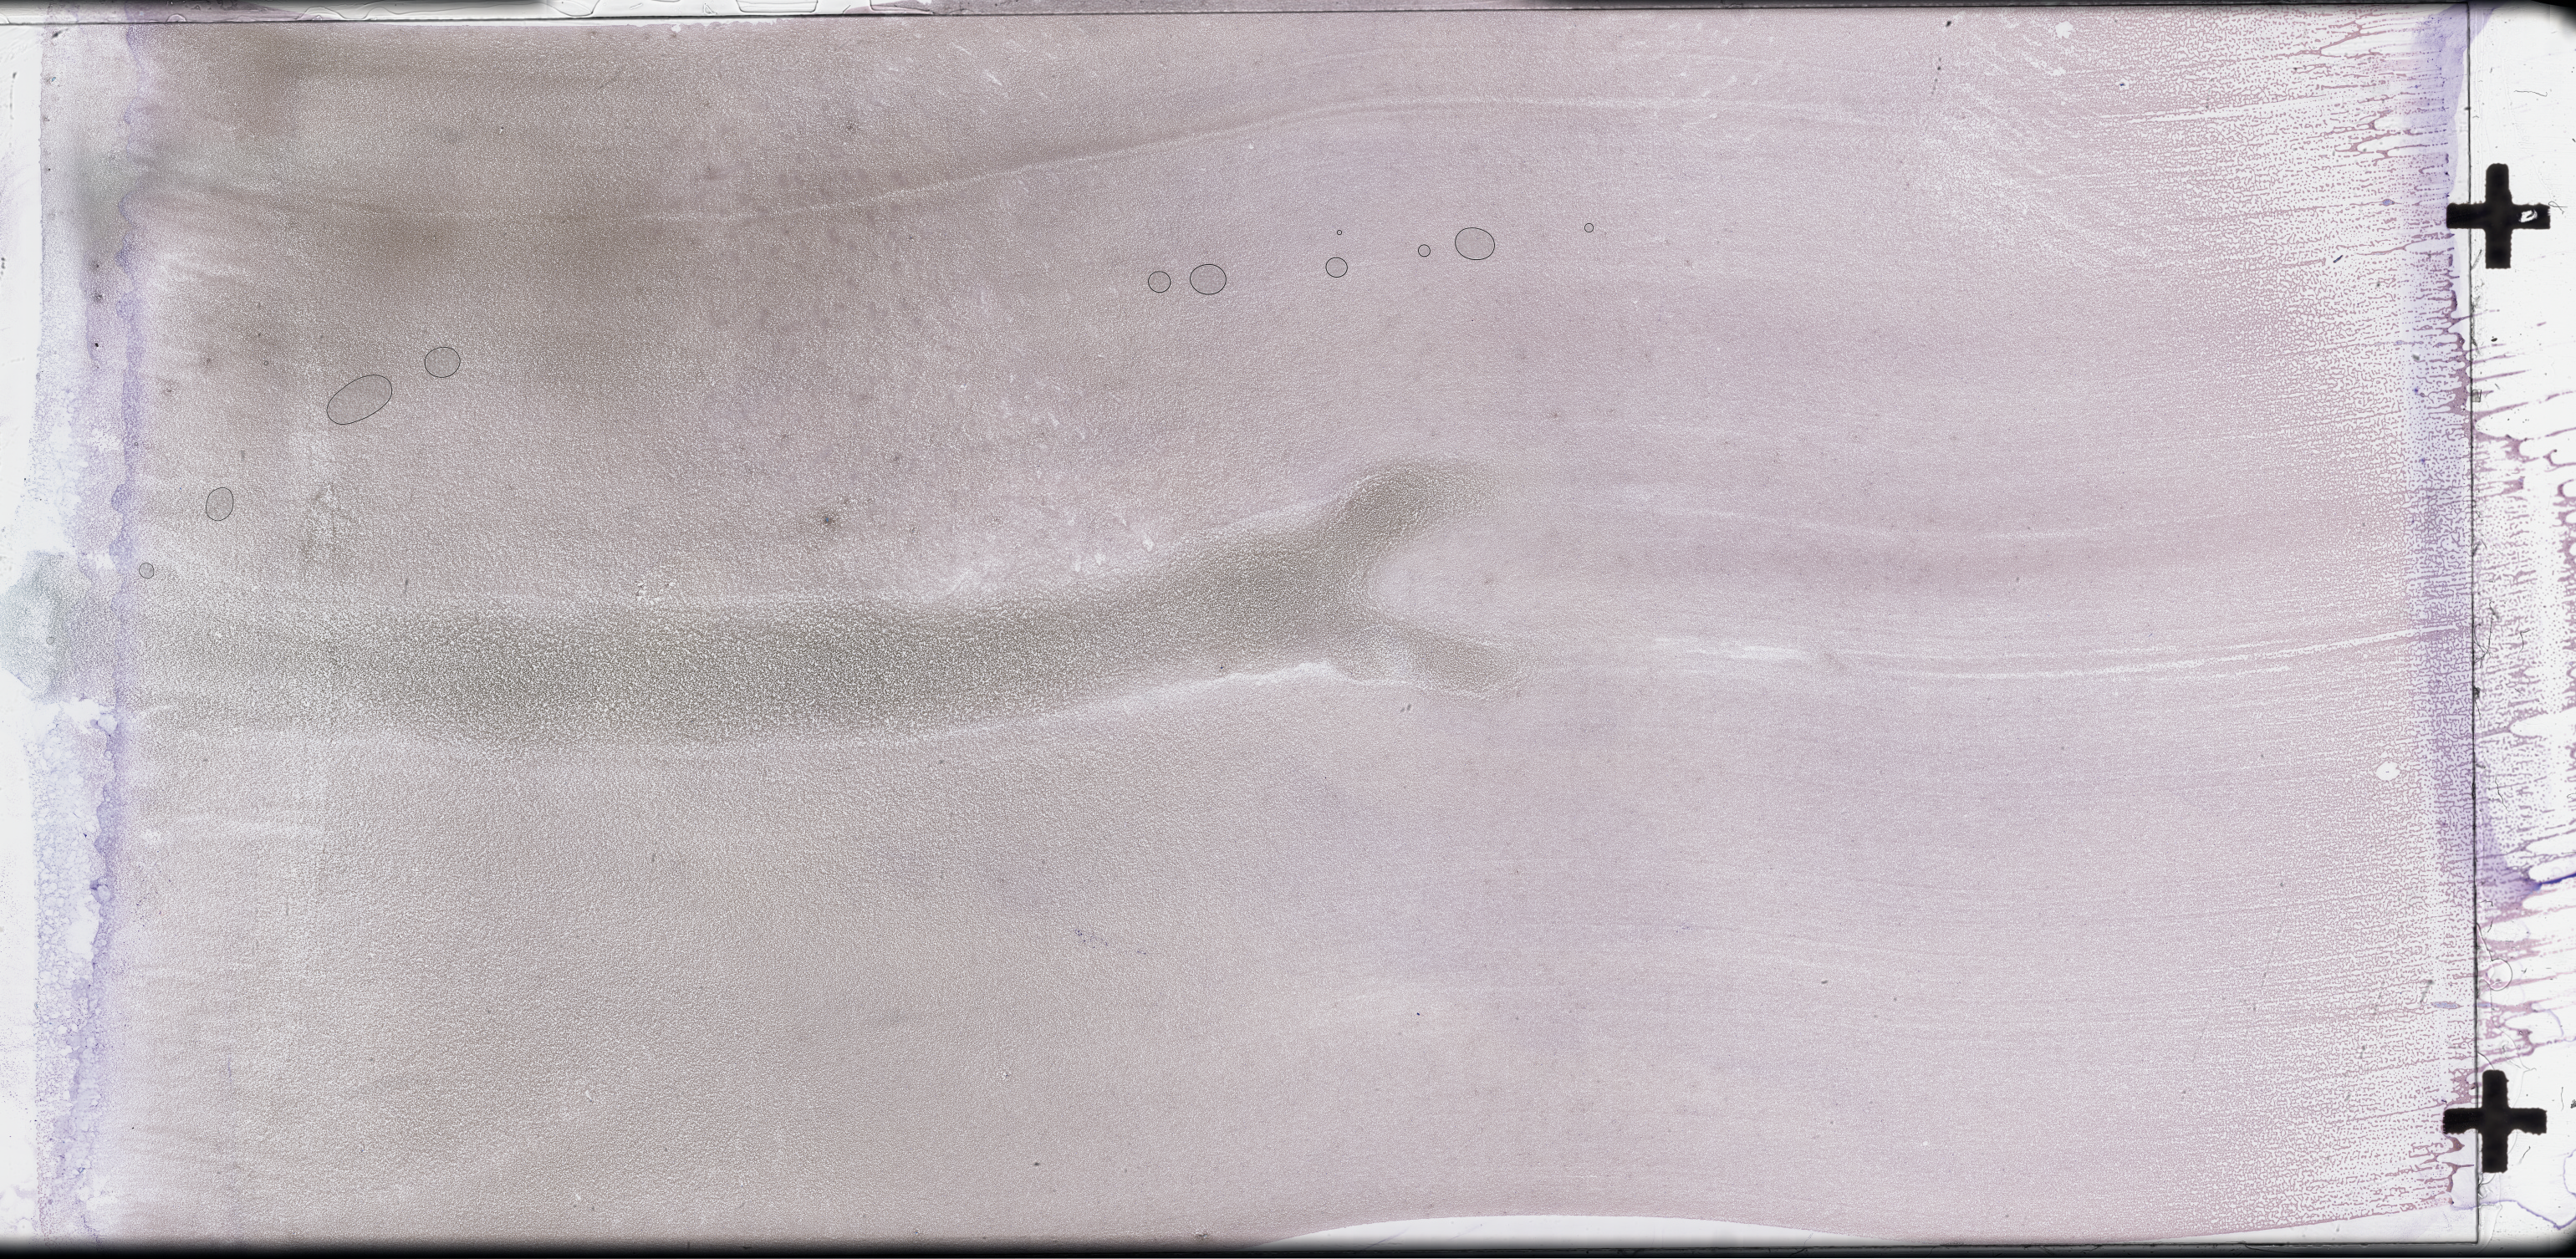
Whole-slide image of a whole blood smear, Wright–Giemsa stain — a low-resolution overview of the entire scanned area, about 49.8 x 24.3 mm, EDTA-anticoagulated smear, collected on treatment. Patient: male.
Patient diagnosis: Plasma Cell Myeloma.